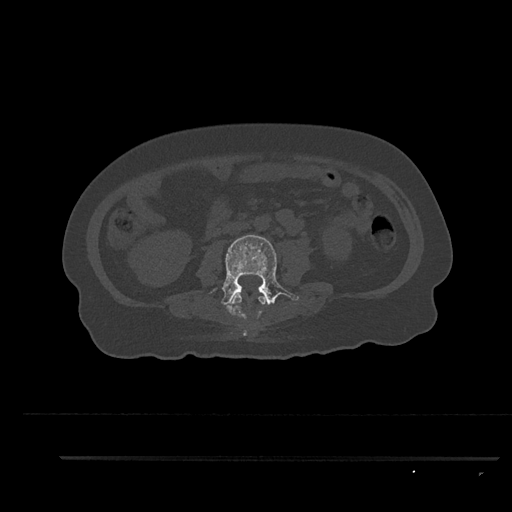
CT including the spine, one axial slice; position 103 of 797 along the scan axis; 120 kVp; bone window (W 1800 / L 400 HU); 0.5 mm slice thickness; 512 × 512 image matrix, field of view 408 × 408 mm. Female patient, age 44 years. From the clinical record (not read from this slice): primary cancer: renal.
Outlined on this slice (semi-automatically segmented with operator editing):
- L2 vertebra: bounding box (x1, y1, x2, y2) in pixels: (231, 293, 266, 319)
- L3 vertebra: (207, 235, 299, 314)